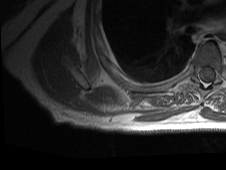
MRI of an extremity soft-tissue mass, one axial slice. MR volume resampled by the dataset authors to the PET/CT grid (not the native acquisition matrix). 226 × 170 image matrix, field of view 221 × 166 mm. Male patient. From the clinical record (not read from this slice): histological type: pleiomorphic spindle cell undifferentiated; grade: high; site of the primary tumour: right parascapusular.
Structures marked on this image (expert contour drawn on MRI and transferred to this co-registered scan by the dataset authors):
- gross tumour volume including surrounding oedema: bounding box <128,104,168,117> (left, top, right, bottom; pixels)